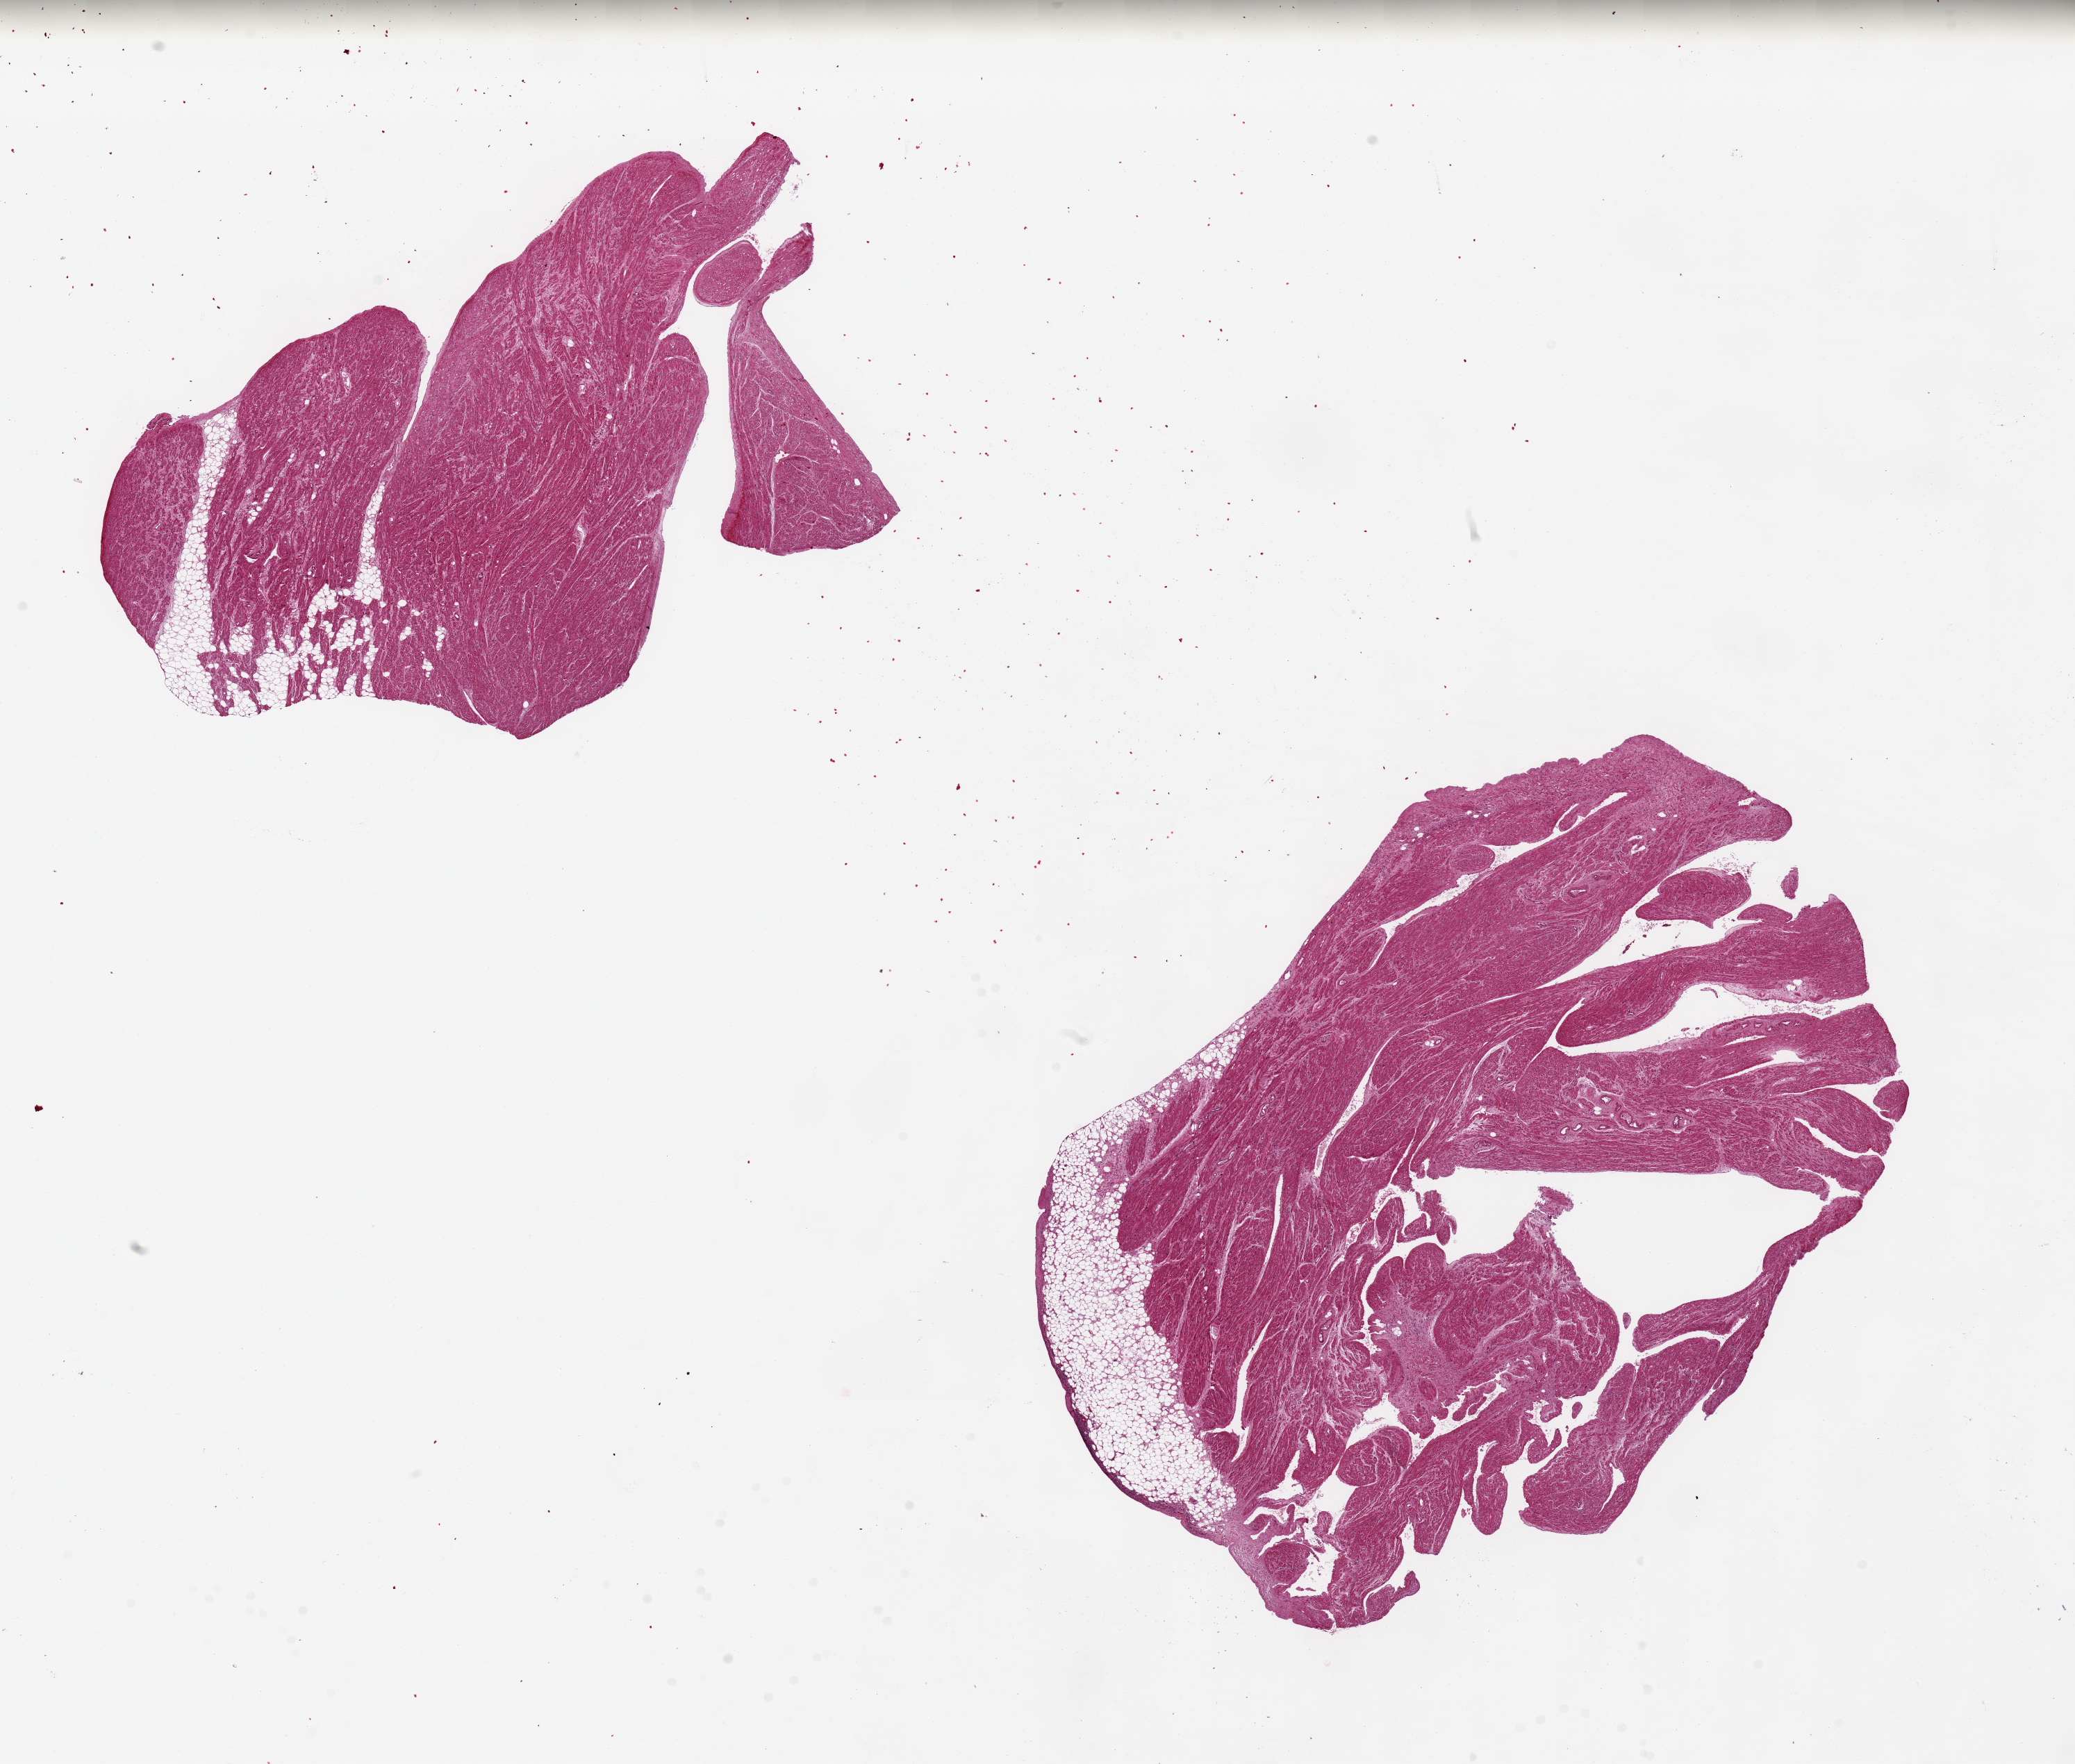
Digitized haematoxylin and eosin-stained section, brightfield — a low-resolution overview of the entire scanned area, about 23.6 x 20.1 mm; PAXgene-fixed paraffin-embedded (PFPE) section; section of auricular appendage (target tissue); tissue donor sample. Donor sex: male.
Pathologist's review note for this sample: 2 pieces, 9x7 & 11x8mm; layer of adherent fat, ~0.5mm.